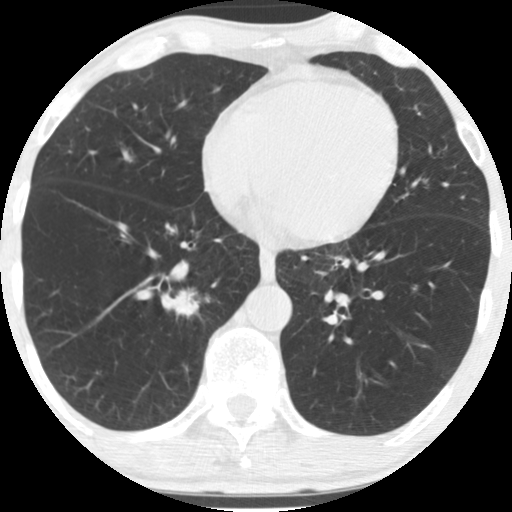
Low-dose screening chest CT, axial slice. Baseline annual screen. Lung window (W 1500 / L -600 HU). 2.5 mm slice thickness. Standard (soft-tissue) reconstruction kernel (STANDARD). 120 kVp. Male, age 67 years at enrolment. Former smoker at enrolment.
• Expert-annotated lung lesion, bounding box (x1, y1, x2, y2) in pixels: (153, 270, 214, 331).
• Screening reader's record for this exam (one nodule recorded; not confirmed to be the boxed lesion): non-calcified nodule or mass ≥4 mm, right lower lobe, 16 × 16 mm, spiculated (stellate) margins, soft tissue attenuation.
• Official screen result: positive, change unspecified: nodule(s) >= 4 mm or enlarging nodule(s), mass(es), or other non-specific abnormalities suspicious for lung cancer.
• Participant outcome: lung cancer diagnosed 49 days after this screen — squamous cell carcinoma, NOS, right lower lobe, moderately differentiated (G2), stage IA (AJCC 6th edition), 20 mm at pathology.